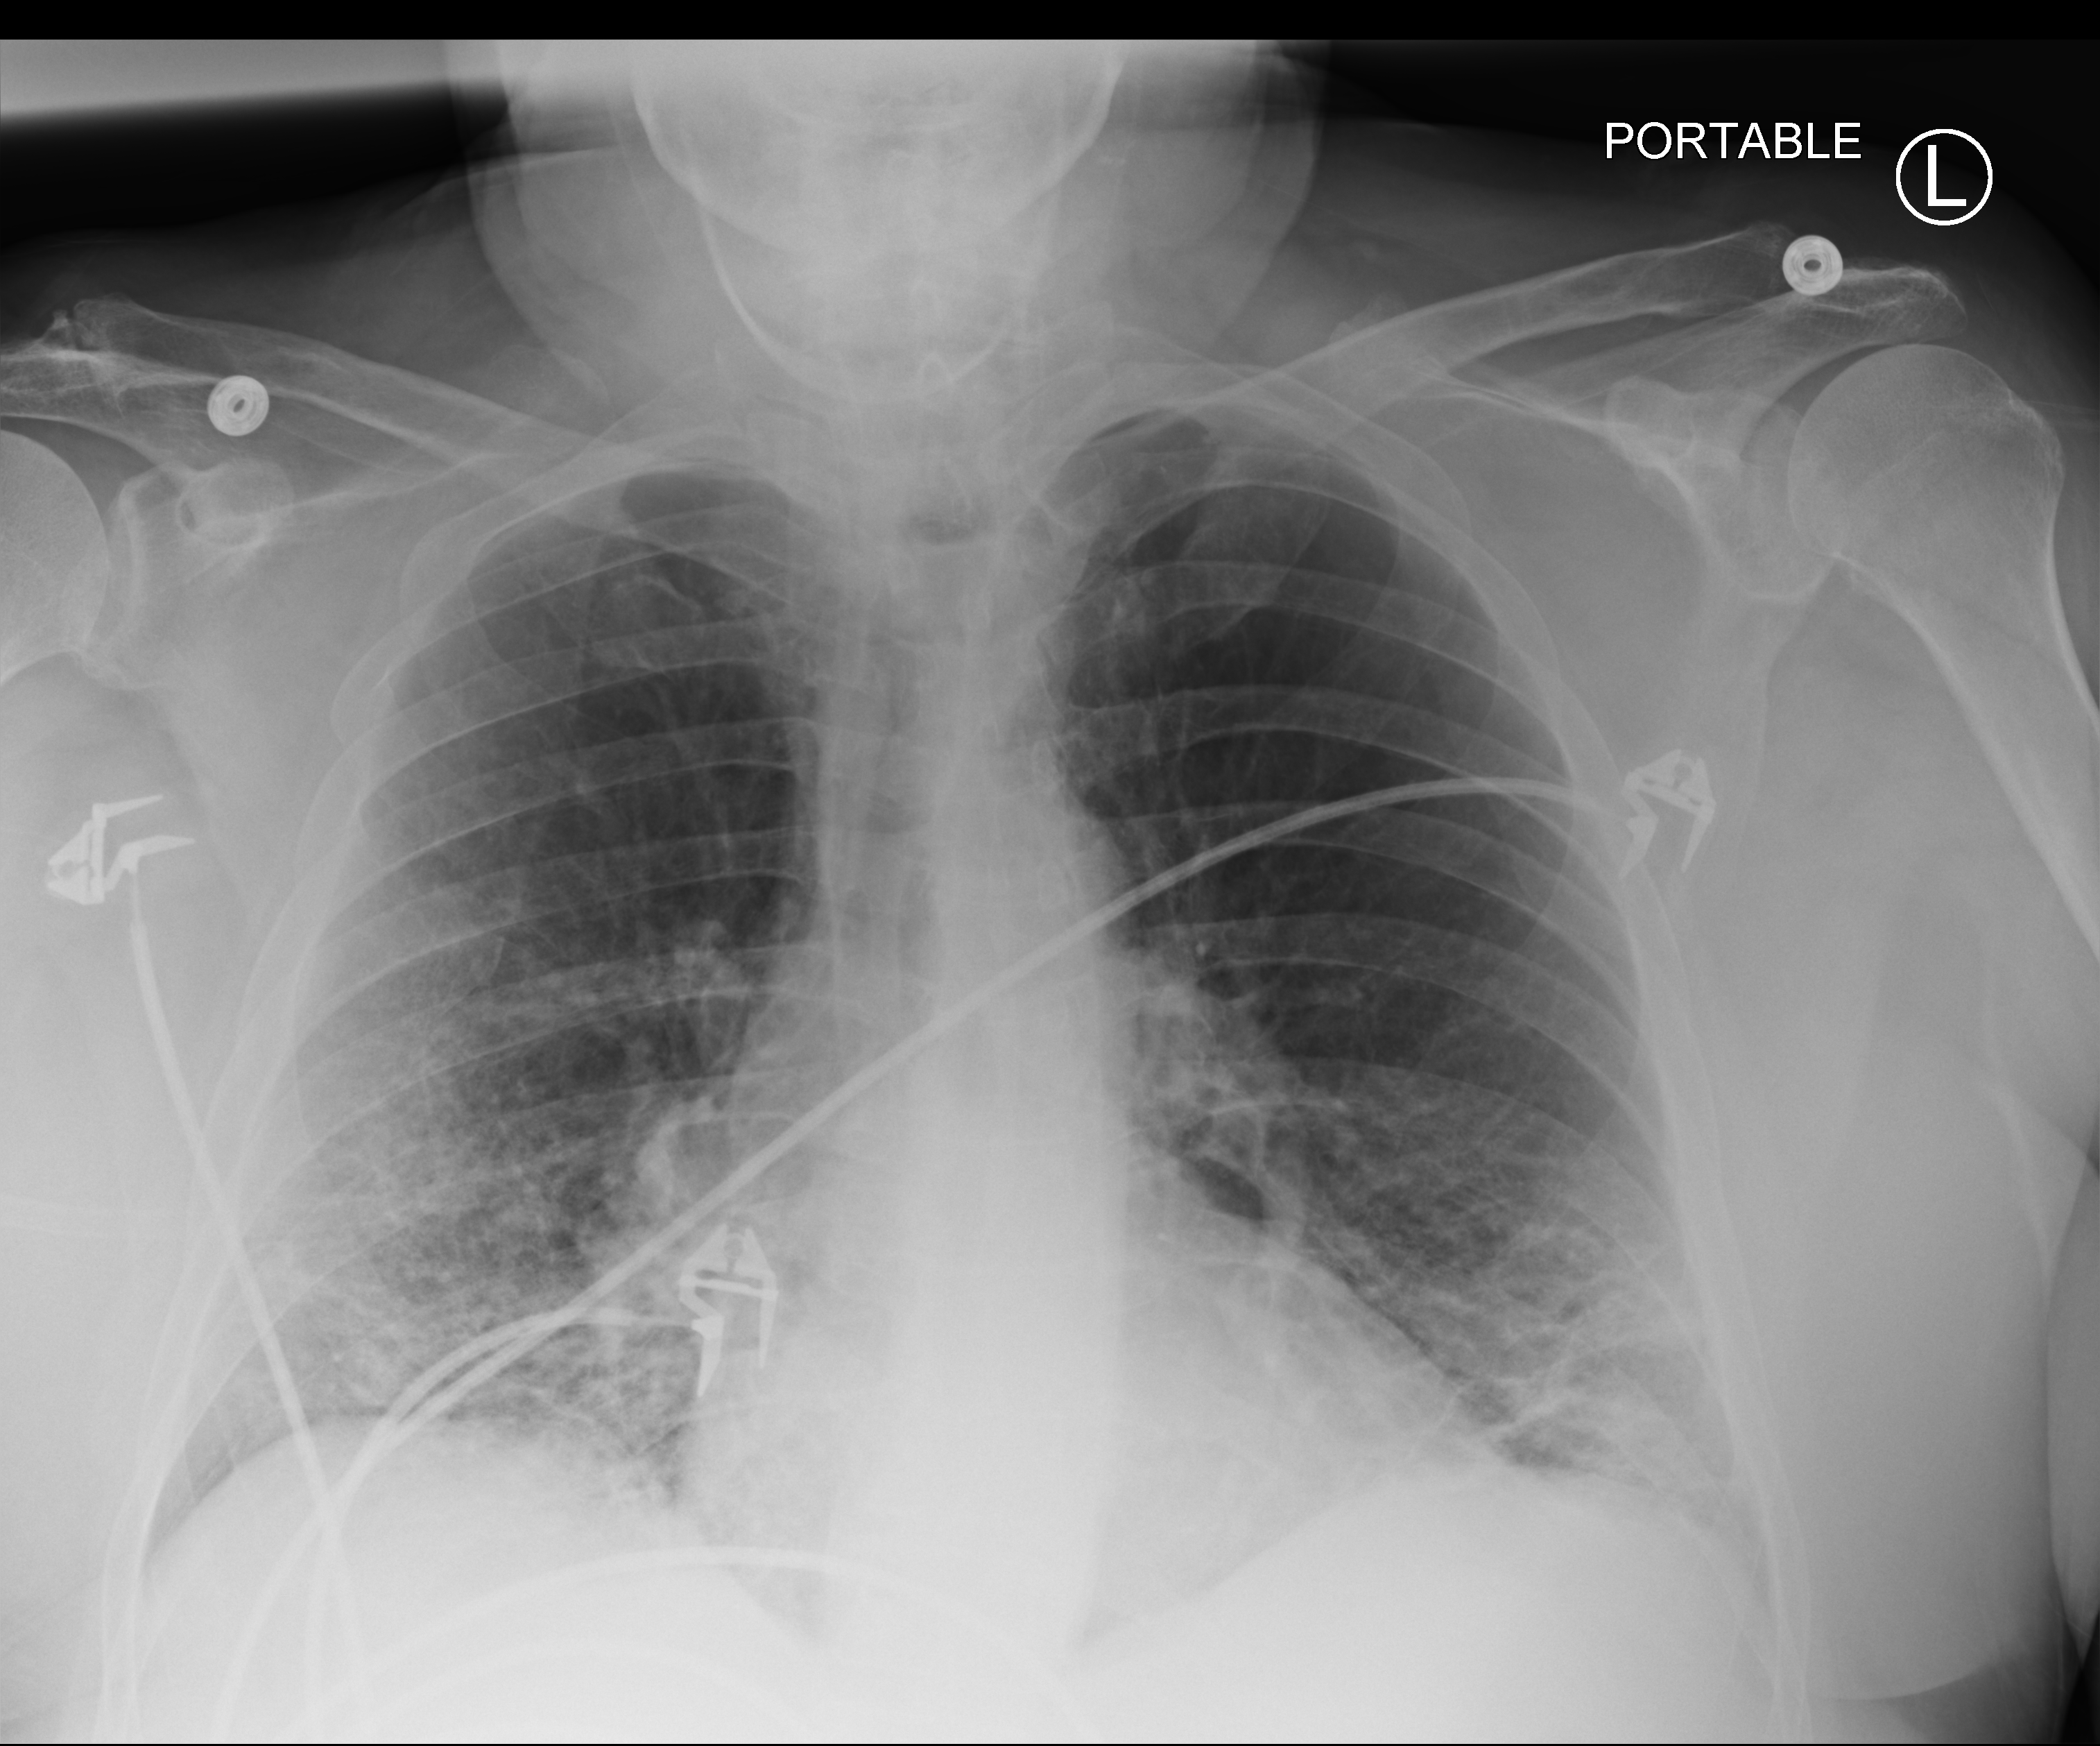
Portable chest radiograph. Patient hospitalised with COVID-19; male, aged 60–74 years.
From the hospital-stay record, not from the radiograph (when in the stay this image was taken is not recorded): mechanically ventilated during this hospital stay: no; diabetes (admission record): no; admitted to intensive care during this hospital stay: no.